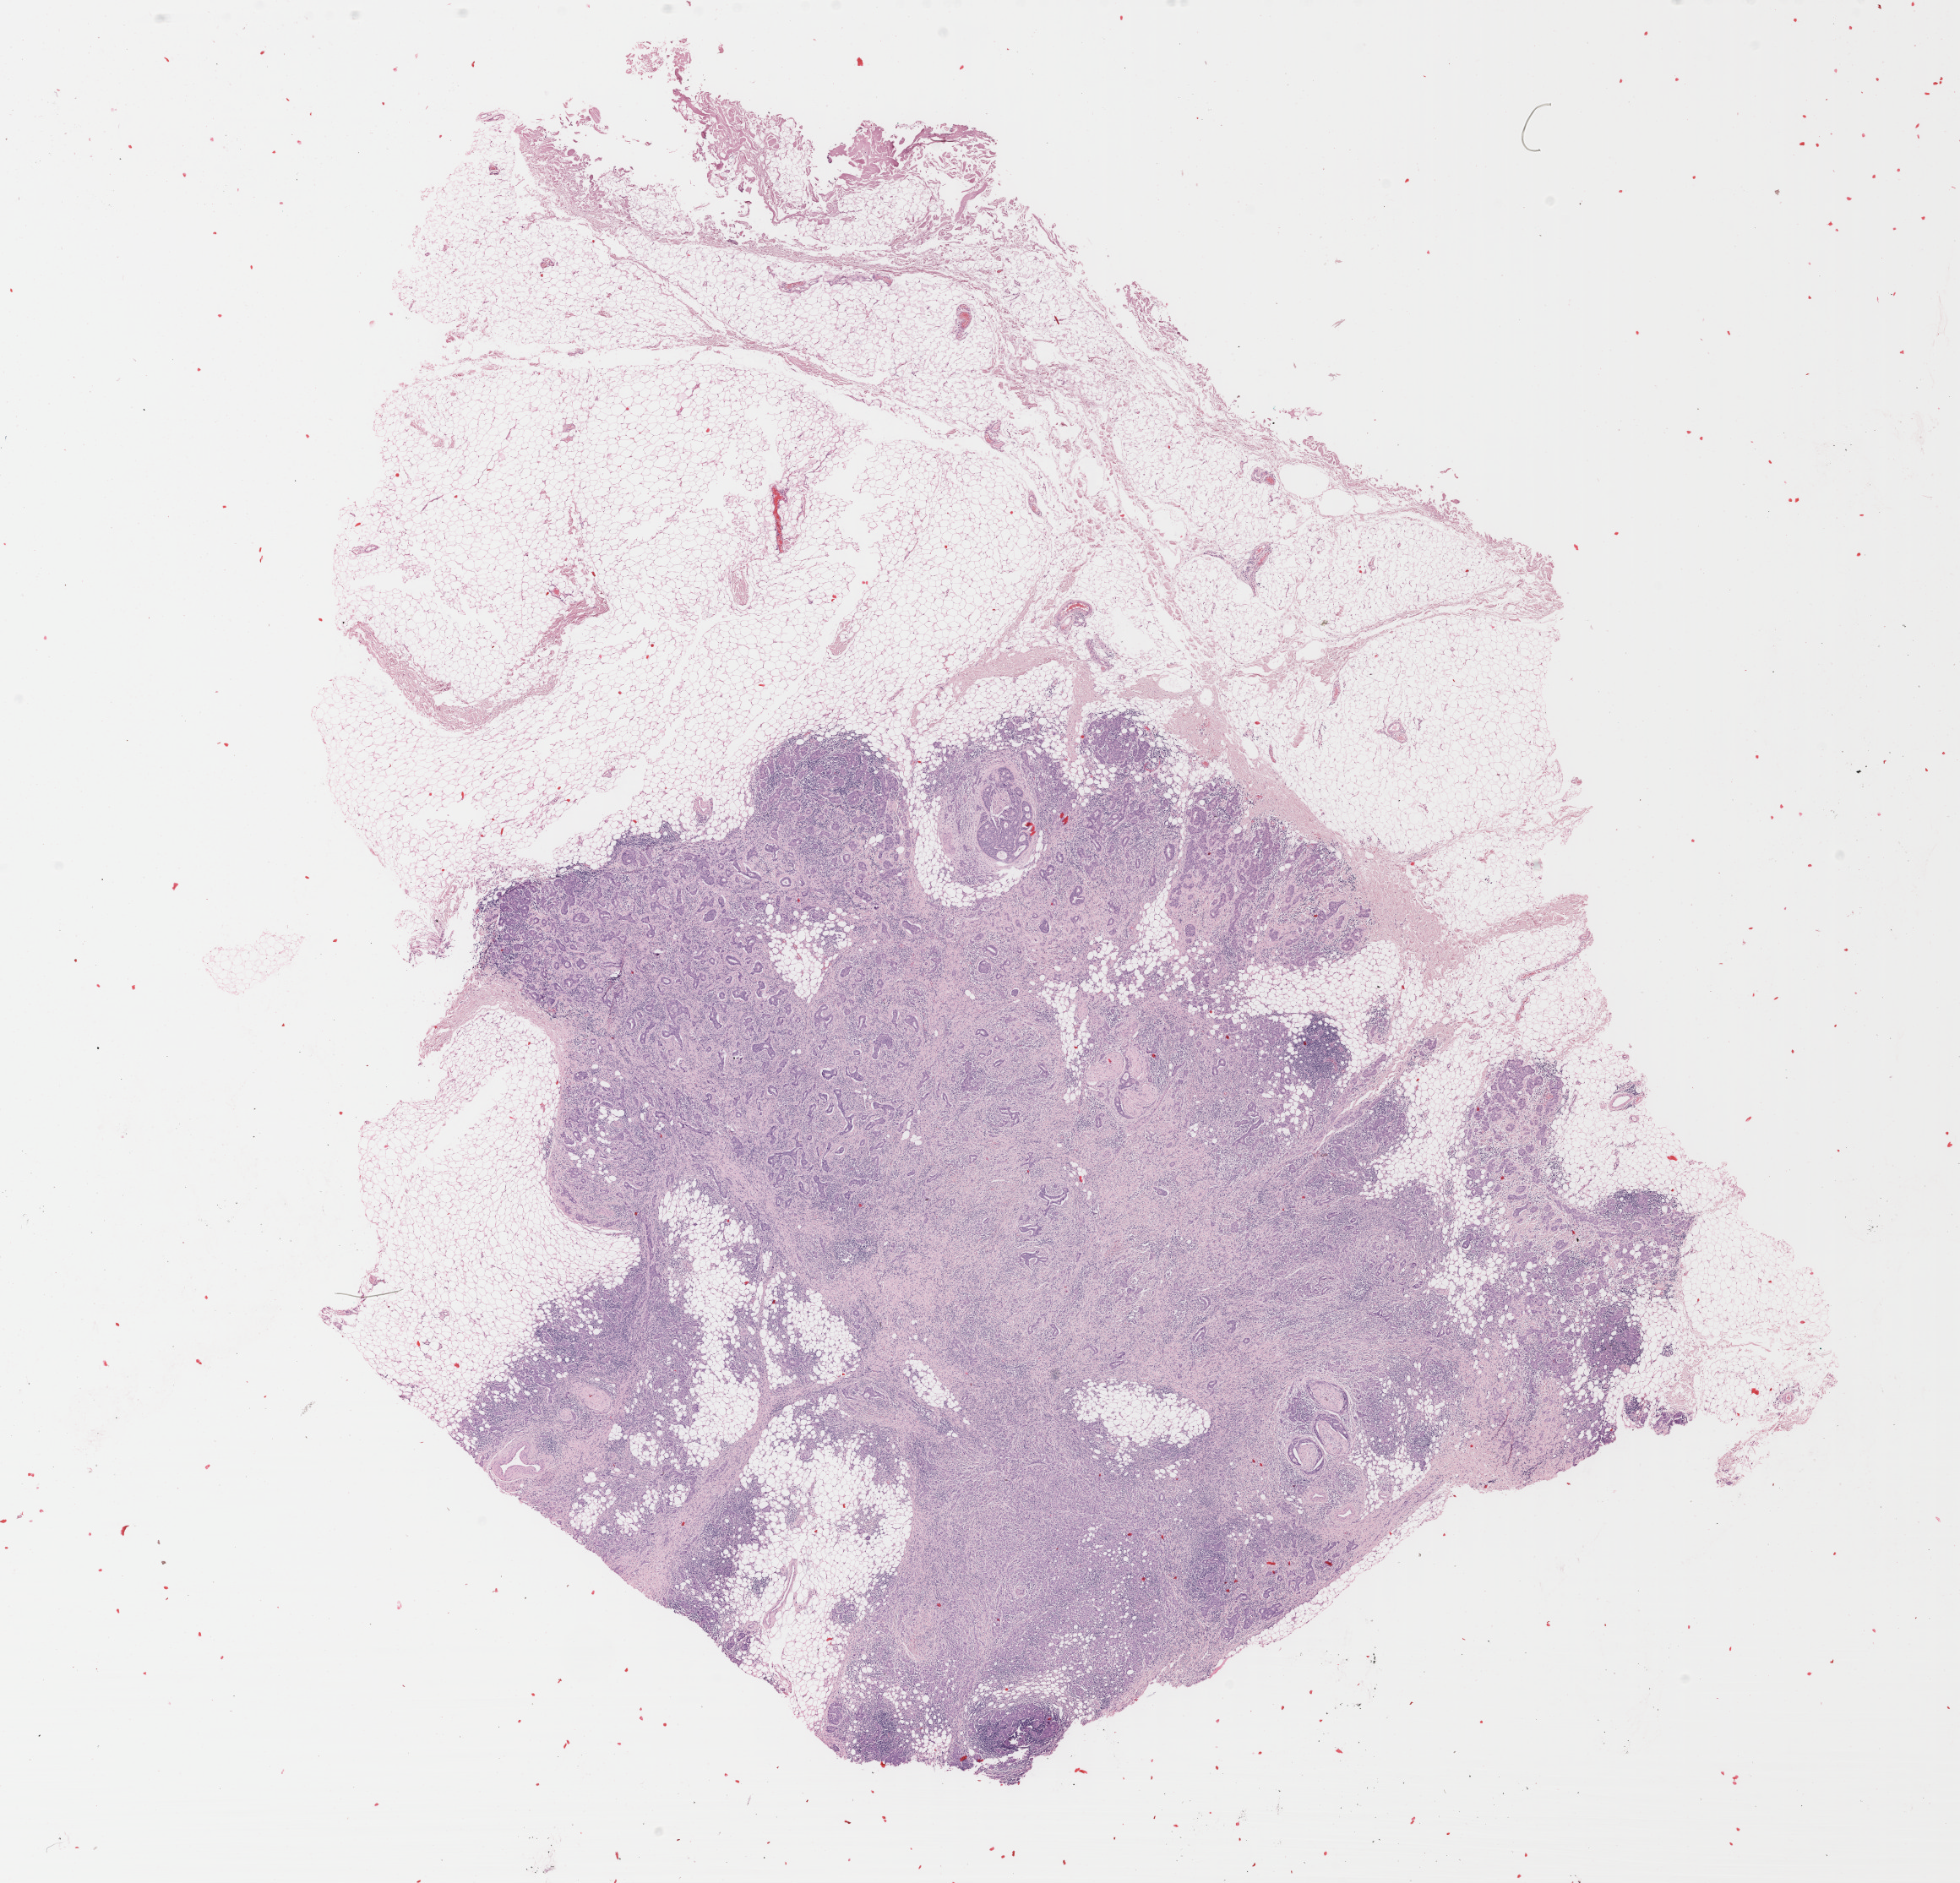
Digitized H&E tissue section (whole slide), low-resolution overview of the scanned area, about 18.4 x 17.7 mm (from a 40x scan). Formalin-fixed paraffin-embedded (FFPE) diagnostic section. Breast, primary tumour sample. Patient: female, age at initial diagnosis 40 years.
- diagnosis: Infiltrating duct carcinoma, NOS